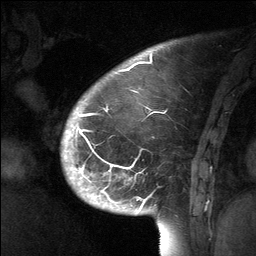
Breast MRI (dynamic contrast-enhanced), one sagittal slice; slice 16 of 64 in the series (ordered by position); dynamic contrast-enhanced study with each time point stored as its own series, time point 2 of 3 at this slice position (early post-contrast, ordered by acquisition time); 1.5 T; TE 4.8 ms, TR 27 ms; 2 mm slice thickness; 256 × 256 image matrix, field of view 200 × 200 mm. Female patient, age 39 years. From the clinical record (not read from this slice): setting: breast cancer imaged before/during neoadjuvant chemotherapy; receptor status: HER2-positive.
Outlined on this slice (semi-automatically segmented with operator editing):
- analysis volume of interest (the breast-tissue region the enhancement analysis was run in; not a lesion): box from (x=70, y=69) to (x=202, y=224) px
- tumour enhancement mask (voxels above the 90 % enhancement threshold inside the analysis volume of interest): (x=79, y=110)–(x=147, y=204)